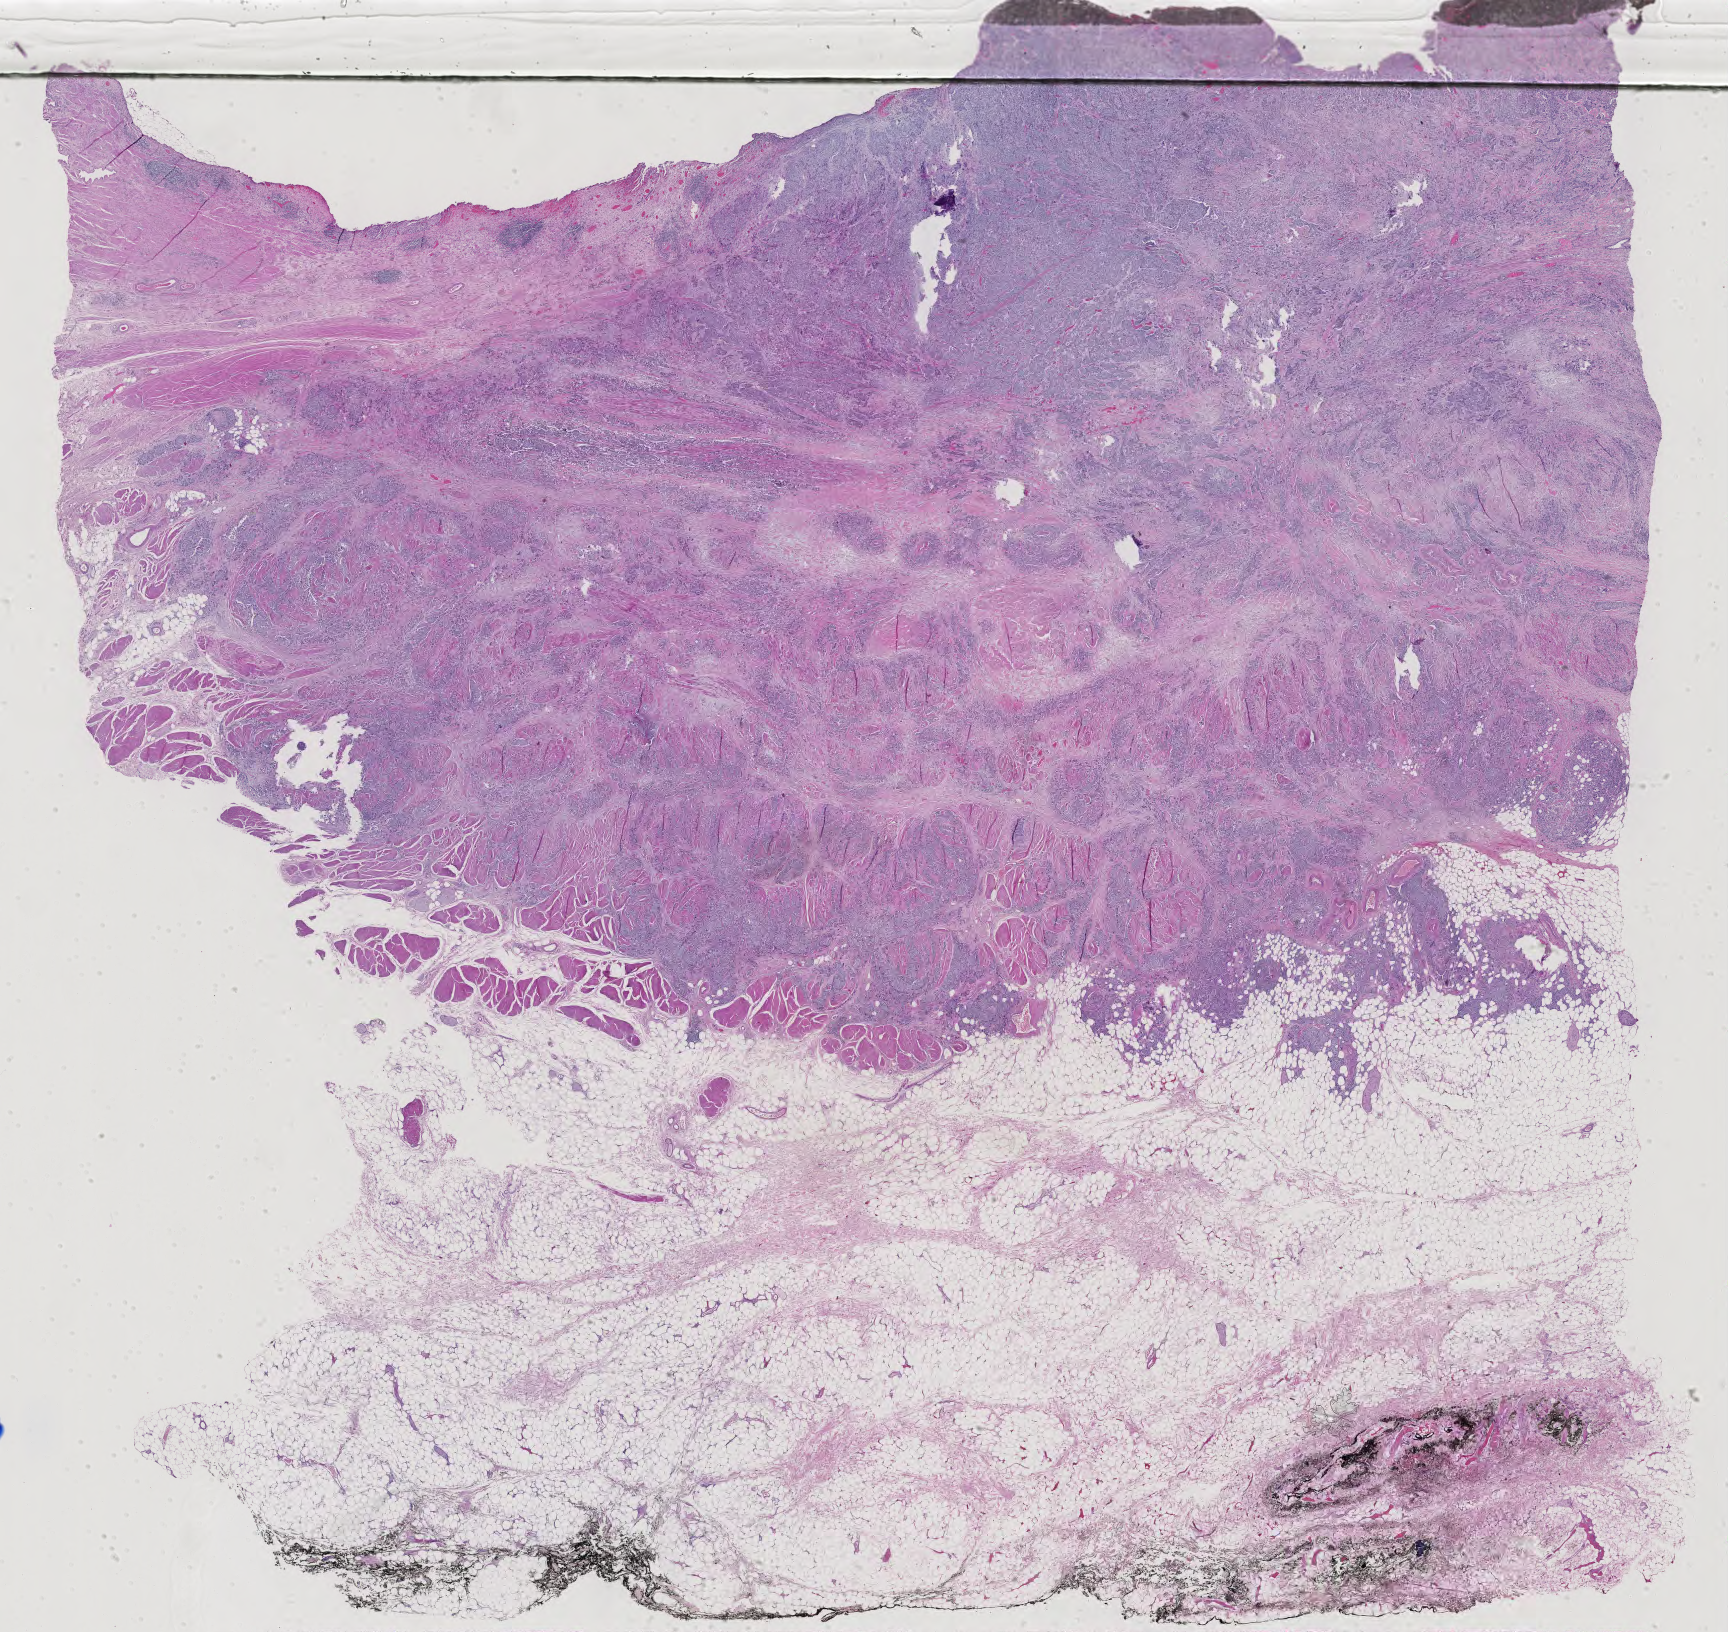
Whole-slide histology image, H&E-stained — whole scanned area (about 25.2 x 23.8 mm) shown as a low-resolution overview. Formalin-fixed paraffin-embedded (FFPE) diagnostic section. Bladder, primary tumour sample. Male patient; age at initial diagnosis 66 years.
Histologic diagnosis: Transitional cell carcinoma (lateral wall of bladder).